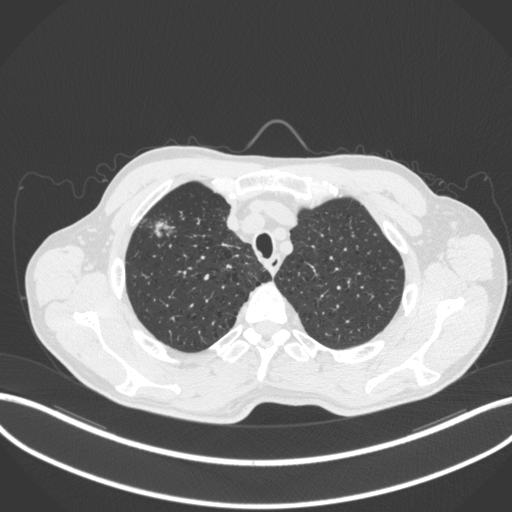
Chest CT, one axial slice; slice 353 of 414 in the series (ordered by position); 120 kVp; lung window (W 1500 / L -600 HU); 1 mm slice thickness; 512 × 512 image matrix. Male patient, age 69 years. Case-level facts recorded for this patient, not image findings: clinical TNM (as recorded): T1b N1 M0.
Structures marked on this image (bounding box drawn by a radiologist):
- lung tumour (recorded histology: adenocarcinoma): bounding box <150,216,176,243> (left, top, right, bottom; pixels)